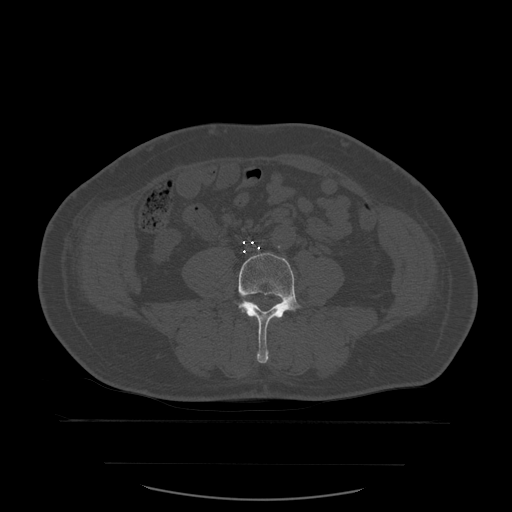
CT including the spine, one axial slice; position 164 of 590 along the scan axis; bone window (W 1800 / L 400 HU); 1.25 mm slice thickness; 512 × 512 image matrix, field of view 479 × 479 mm. Patient age 71 years. Case-level facts recorded for this patient, not image findings: primary cancer: lung; vertebrae with lytic lesions (as recorded): T1, T2, L5, S1.
Structures marked on this image (semi-automatically segmented with operator editing):
- L4 vertebra: bounding box <238,253,301,364> (left, top, right, bottom; pixels)
- L5 vertebra: <251,302,254,304>